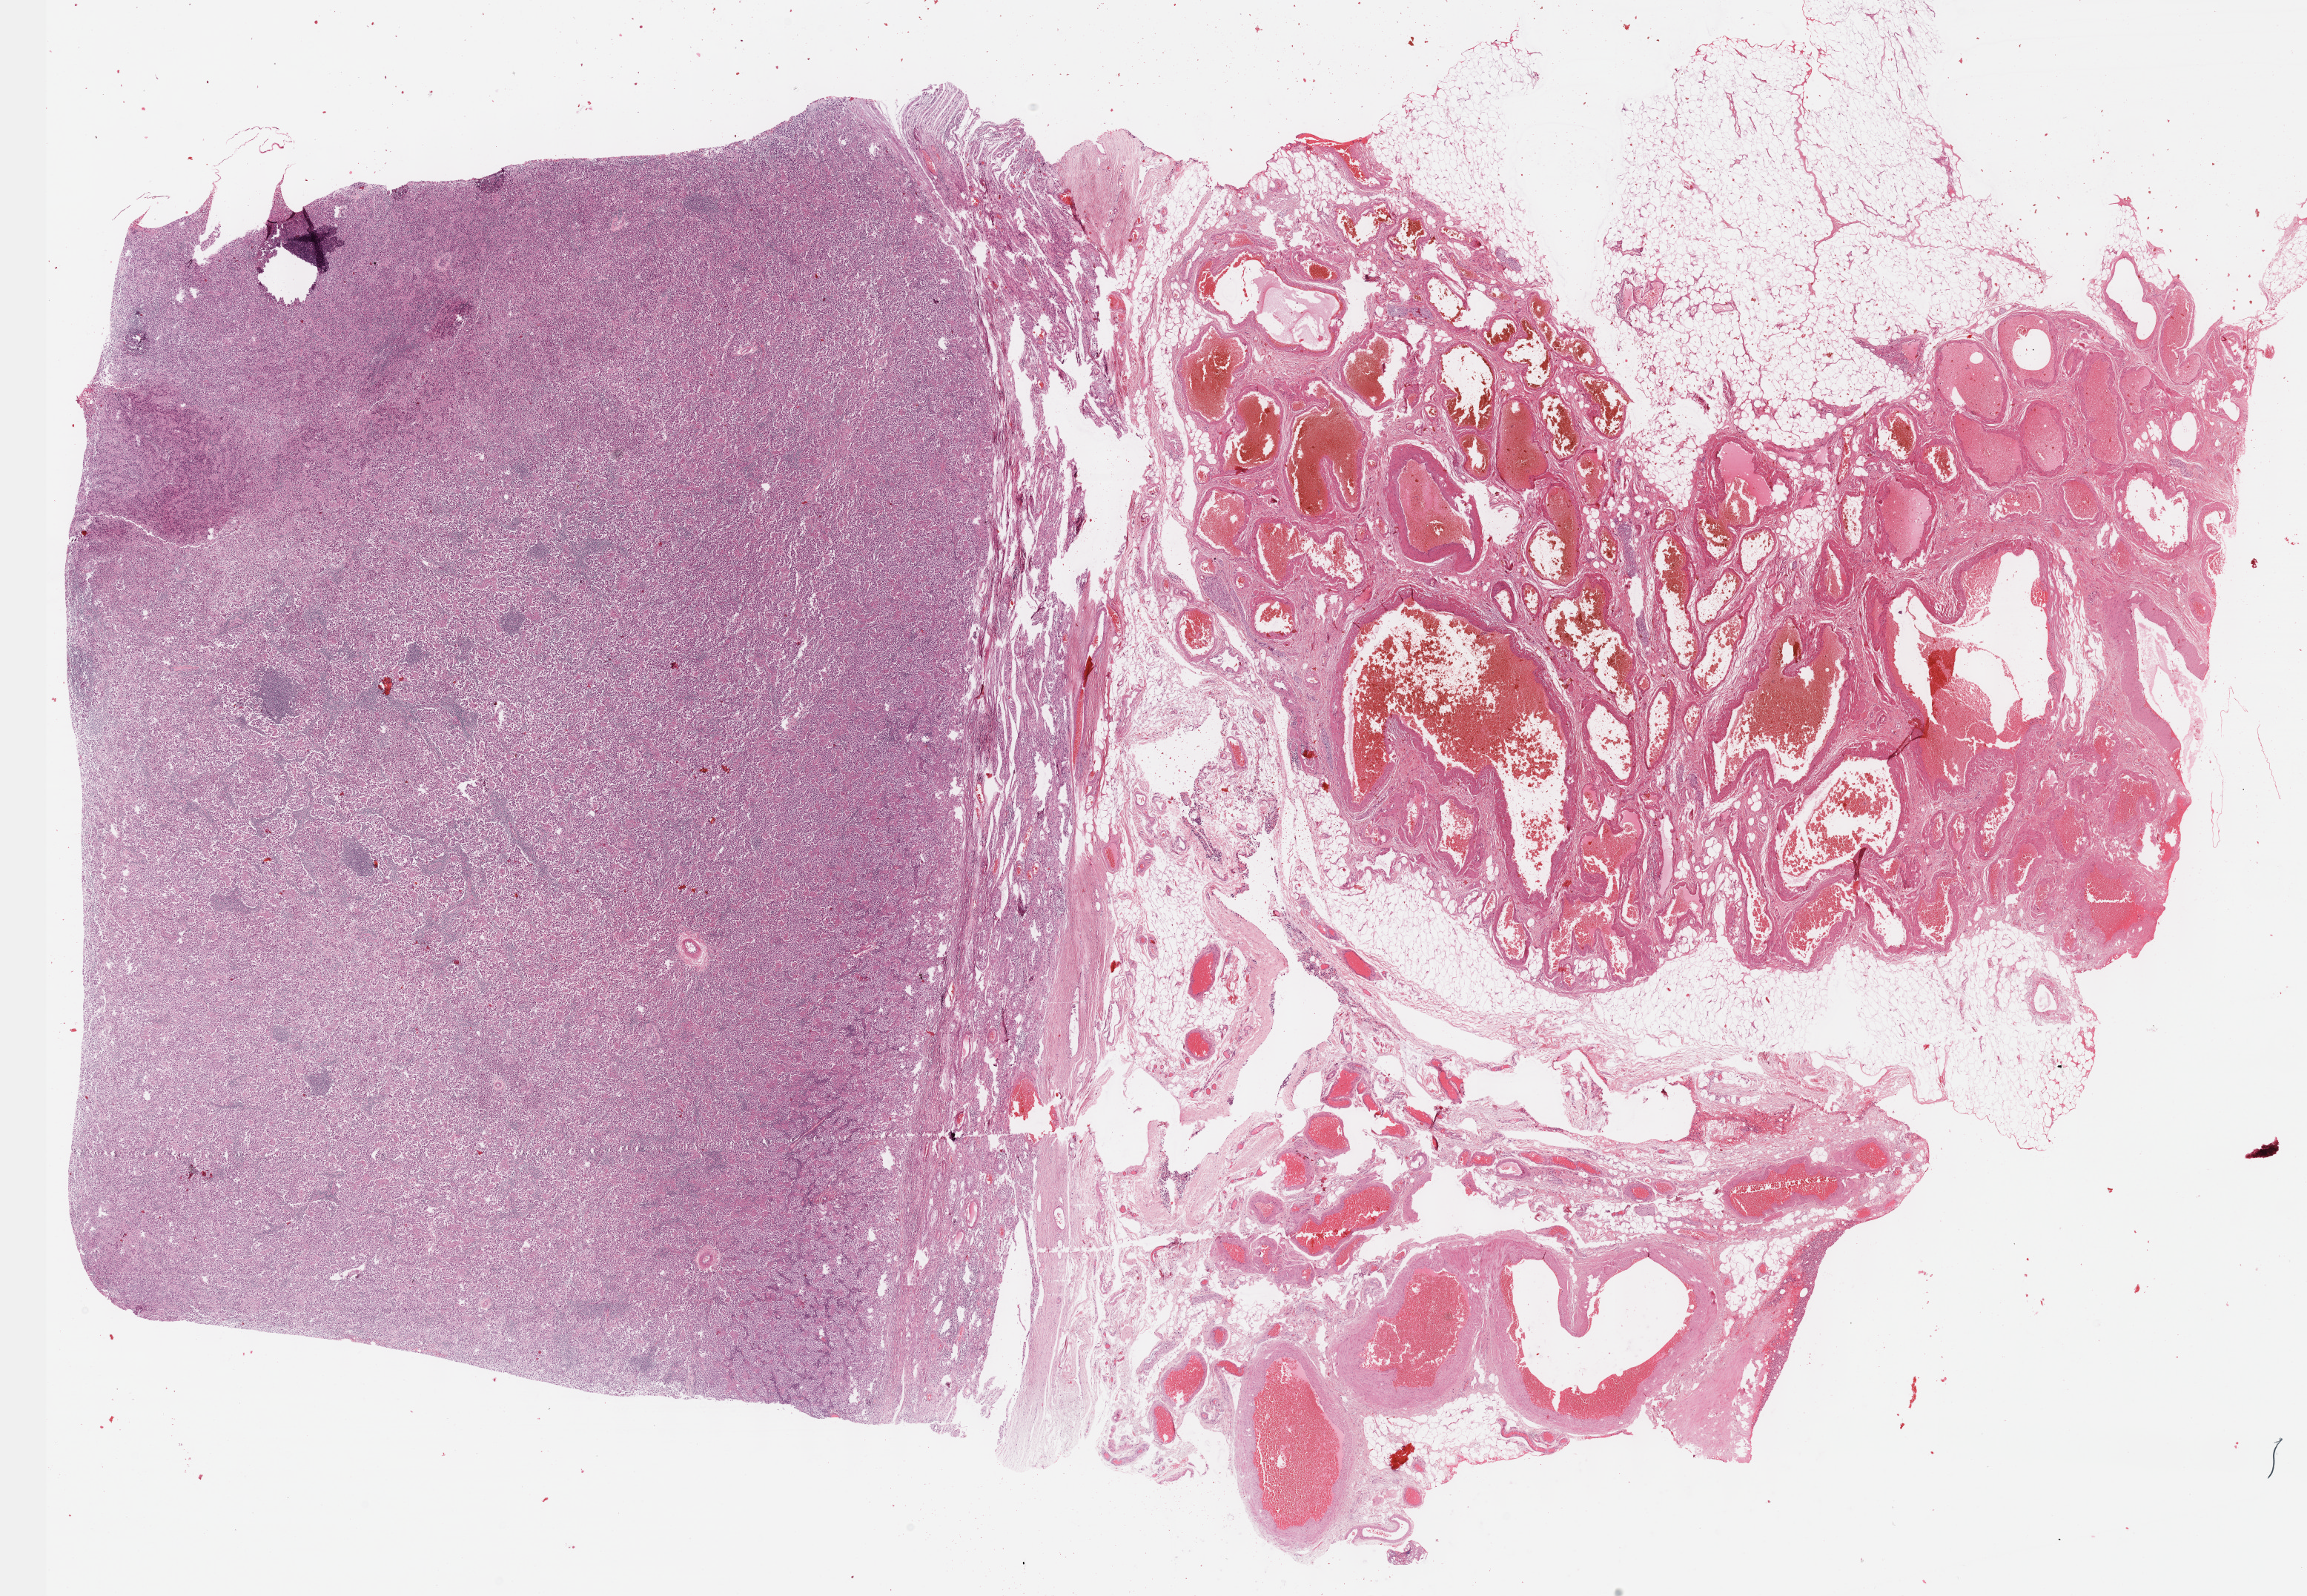
H&E-stained whole-slide image — low-resolution overview of the scanned area, about 25.1 x 17.4 mm (slide scanned at 40x), formalin-fixed paraffin-embedded (FFPE) diagnostic section, testis, primary tumour sample. Male patient; age at initial diagnosis 39 years.
Laterality: bilateral. AJCC pathologic stage: IA (7th edition). Histologic diagnosis: Seminoma, NOS.